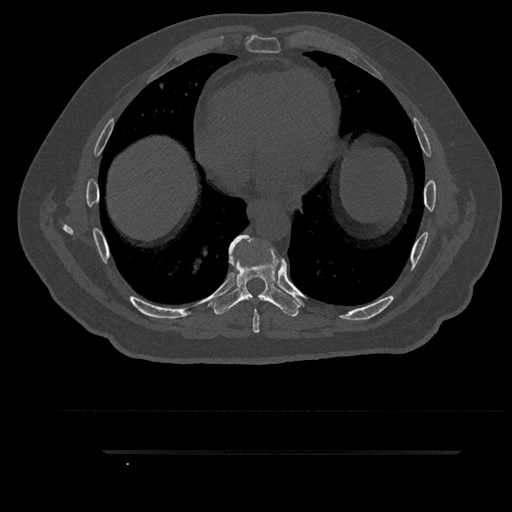
CT including the spine, one axial slice; position 493 of 797 along the scan axis; reconstruction kernel Br40s/3; 120 kVp; bone window (W 1800 / L 400 HU); 512 × 512 image matrix. Male patient, age 63 years. From the clinical record (not read from this slice): primary cancer: renal; vertebrae with lytic lesions (as recorded): T8.
Outlined on this slice (semi-automatic segmentation, software-assisted and operator-edited):
- T7 vertebra: bounding box <236,236,284,333> (left, top, right, bottom; pixels)
- T8 vertebra: <208,235,301,317>